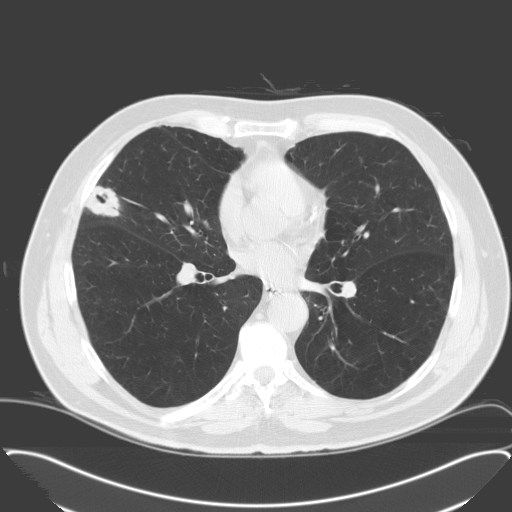
Low-dose screening chest CT, one axial slice. Position 88 of 174 along the scan axis. Lung window (W 1500 / L -600 HU). 3.2 mm slice thickness. 512 × 512 image matrix.
Outlined on this slice (outlined manually by an expert reader):
- lesion 1 (tumor, middle lobe of right lung): bounding box (x1, y1, x2, y2) in pixels: (85, 186, 119, 217)